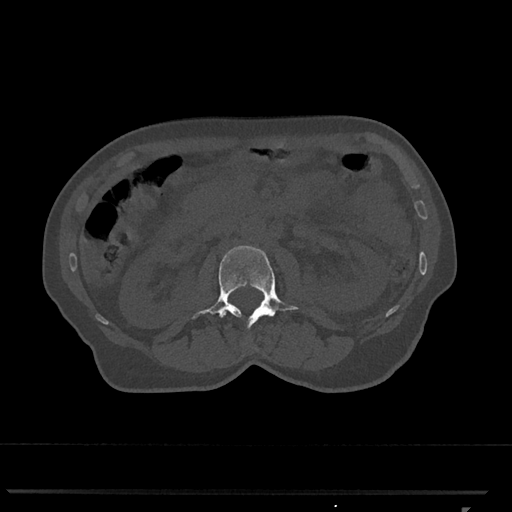
CT including the spine, one axial slice. Slice 342 of 793 in the series (ordered by position). Reconstruction kernel Br40s/3. 120 kVp. Bone window (W 1800 / L 400 HU). 0.5 mm slice thickness. 512 × 512 image matrix, field of view 380 × 380 mm. Female patient, age 62 years. From the clinical record (not read from this slice): primary cancer: renal.
Outlined on this slice (semi-automatic segmentation, software-assisted and operator-edited):
- L2 vertebra: bounding box <192,245,299,328> (left, top, right, bottom; pixels)